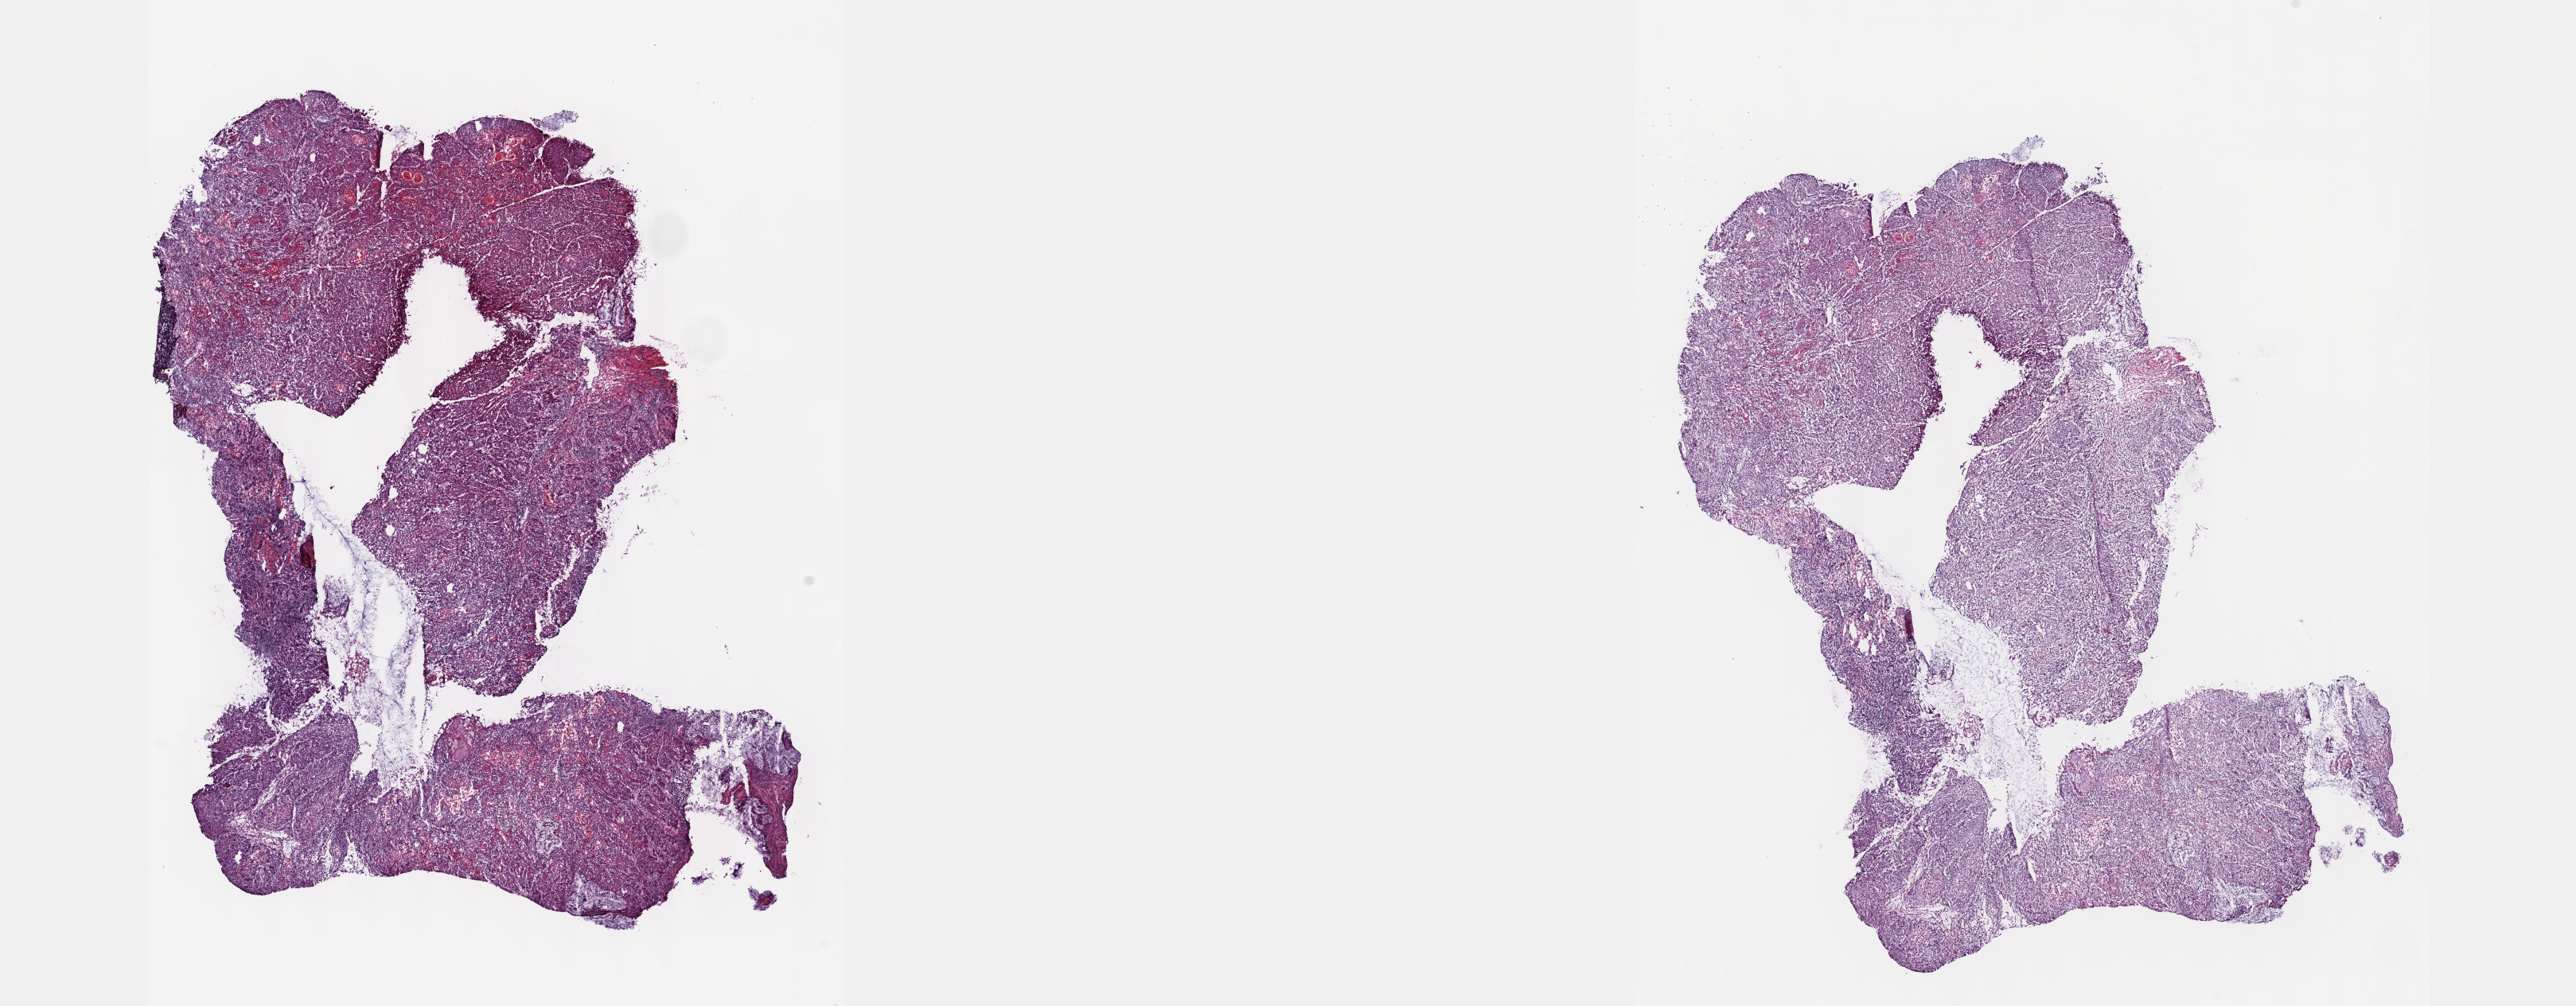
H&E-stained whole-slide image, low-resolution overview of the scanned area, about 26.2 x 10.2 mm (from a 40x scan), frozen section, sample: primary tumour, cervix. Female, age 26 years at initial diagnosis. Histologic grade: G2 (moderately differentiated). Slide review estimates, as recorded: tumour cells 70%, tumour nuclei 70%, normal cells 0%, stromal cells 25%, necrosis 5%. Infiltration values recorded for this section: lymphocyte infiltration 40%, monocyte infiltration 20%, neutrophil infiltration 20%.
FIGO stage: IB. Diagnosis: Squamous cell carcinoma, NOS (cervix uteri).